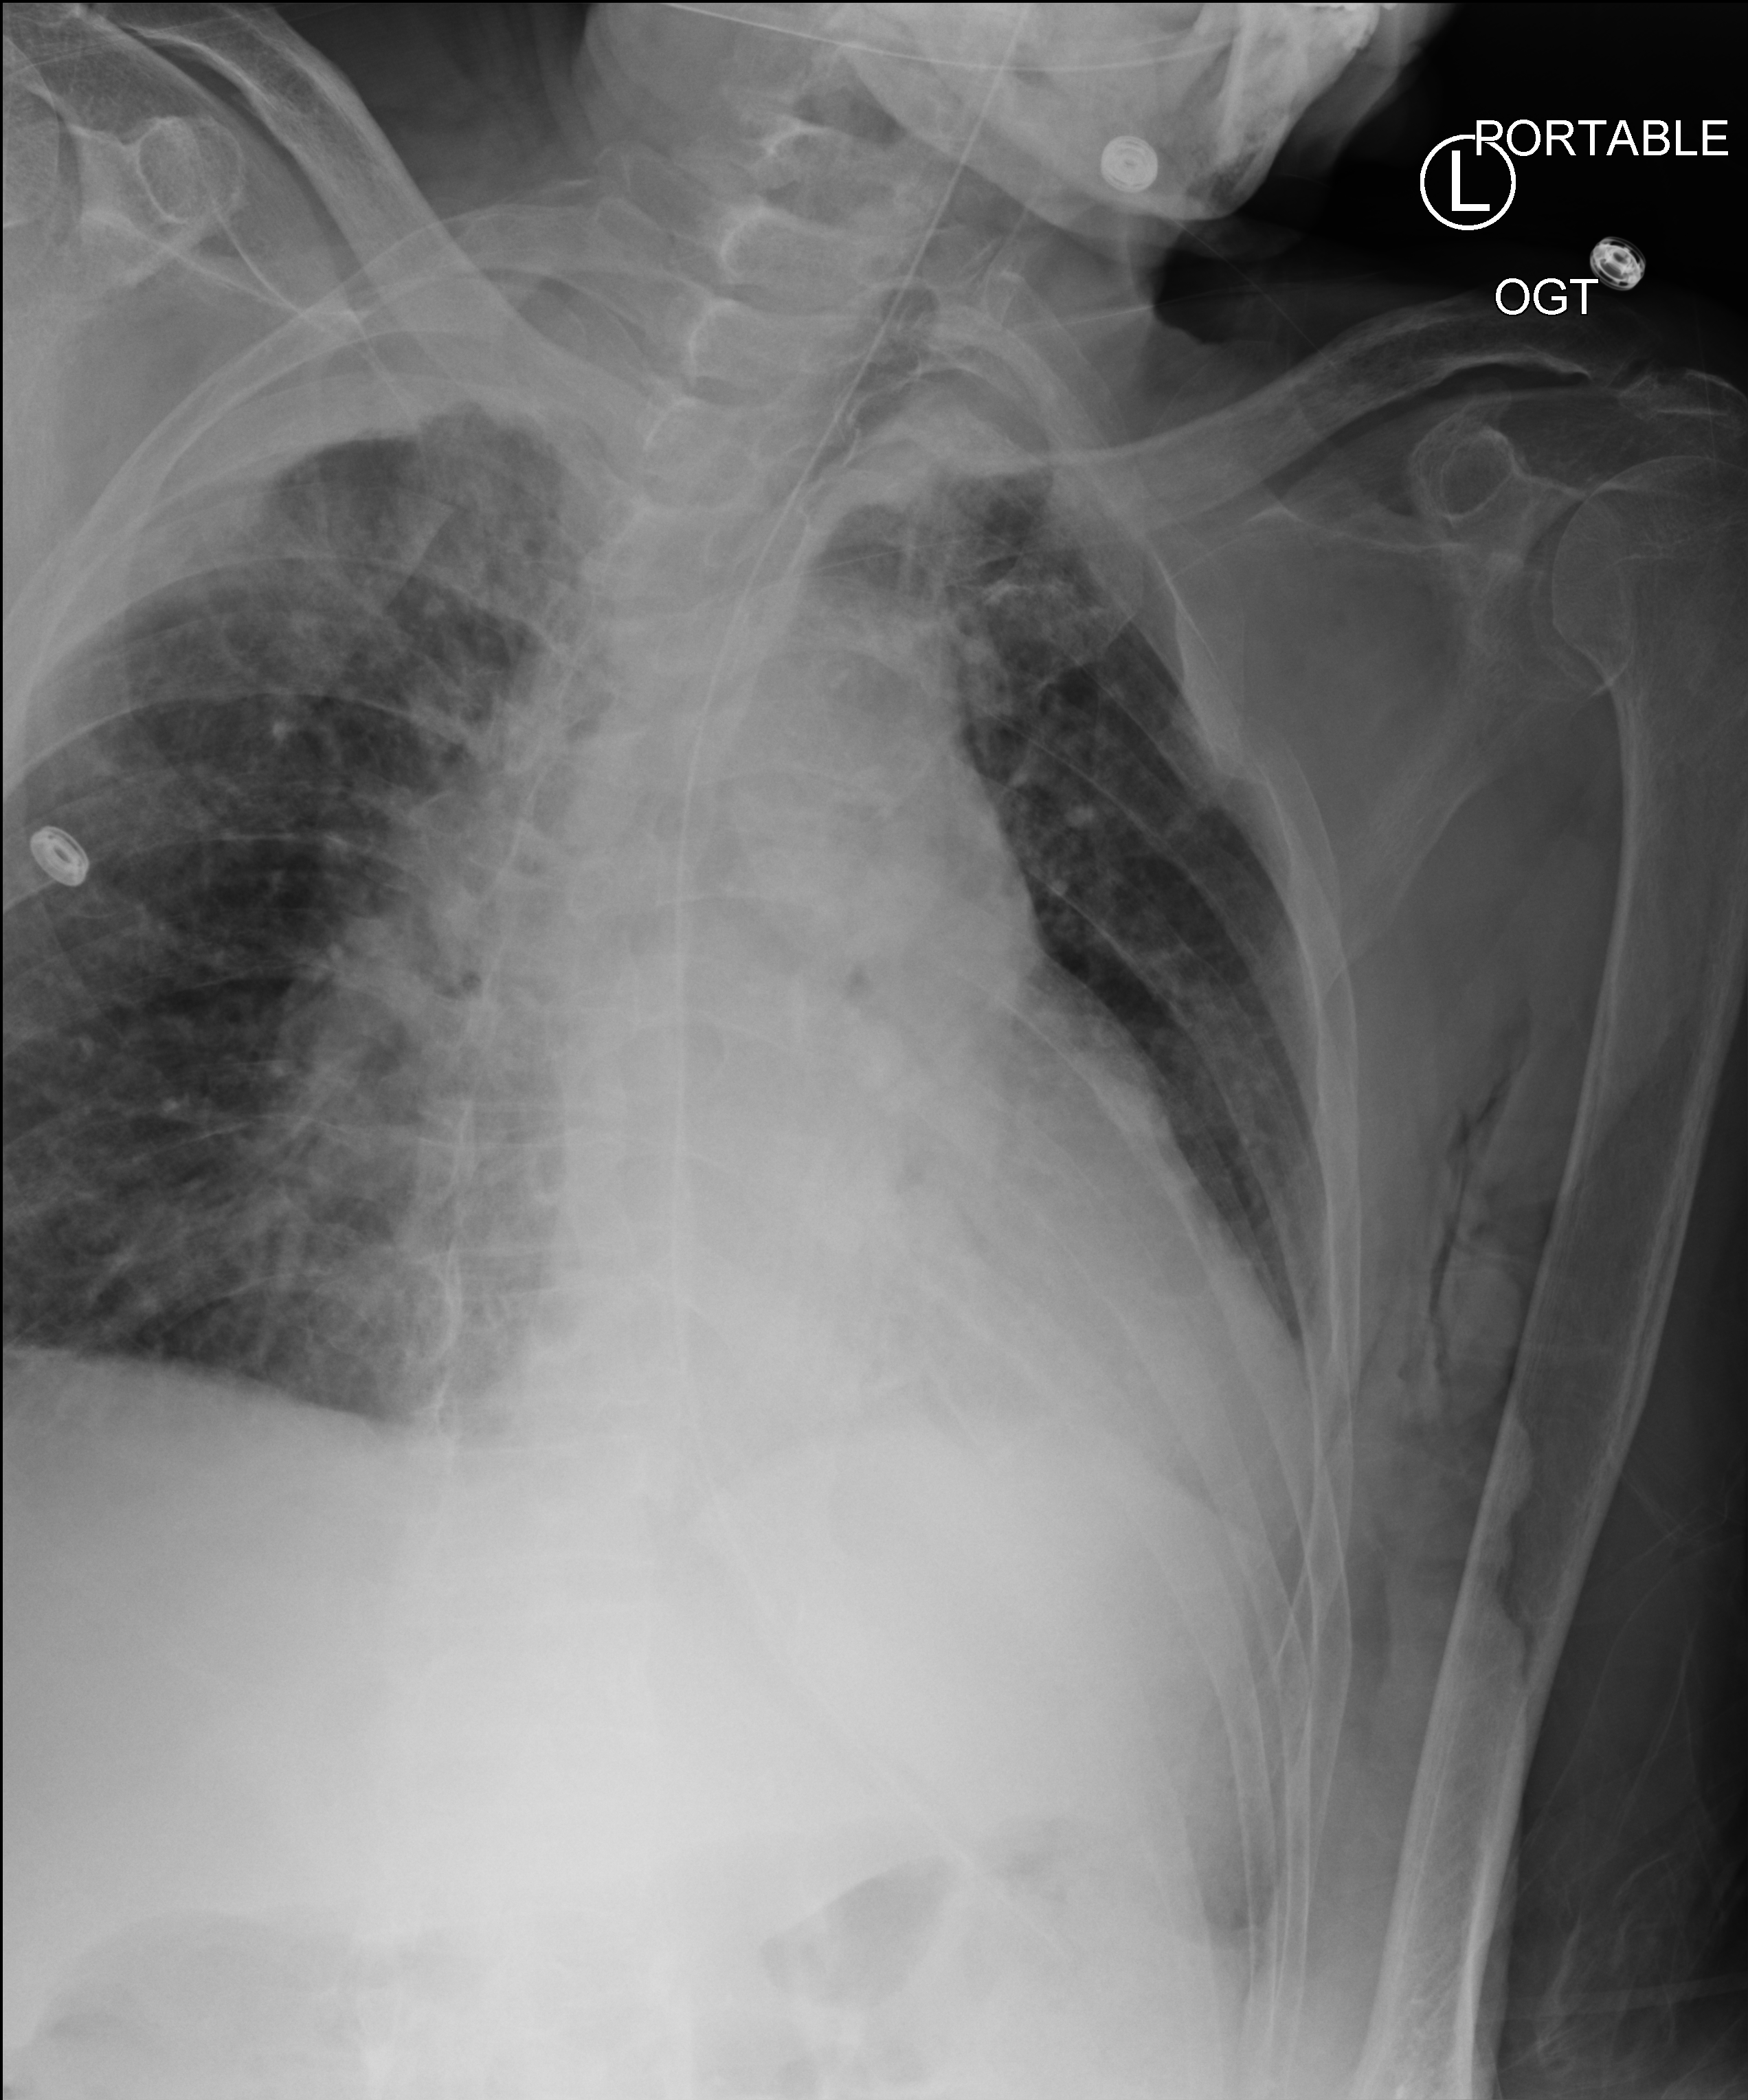
Chest X-ray (portable); anteroposterior (AP) projection. Male patient hospitalised with COVID-19, age 75–90 years.
Admission-level facts for this patient (not findings on this image; timing relative to this image not recorded): diabetes (admission record): no; mechanically ventilated during this hospital stay: no.